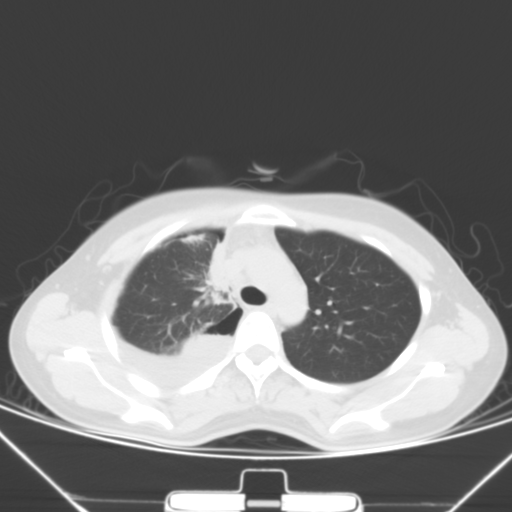
Chest CT, one axial slice. Slice 41 of 57 in the series (ordered by position). 120 kVp. Lung window (W 1500 / L -600 HU). 5 mm slice thickness. 512 × 512 image matrix. Patient: female, 28 years. Case-level facts recorded for this patient, not image findings: clinical TNM (as recorded): T2 N0 M1a.
Annotated regions visible in this slice (rectangle marked by the reading radiologist):
- lung tumour (recorded histology: adenocarcinoma): box from (x=201, y=233) to (x=238, y=296) px